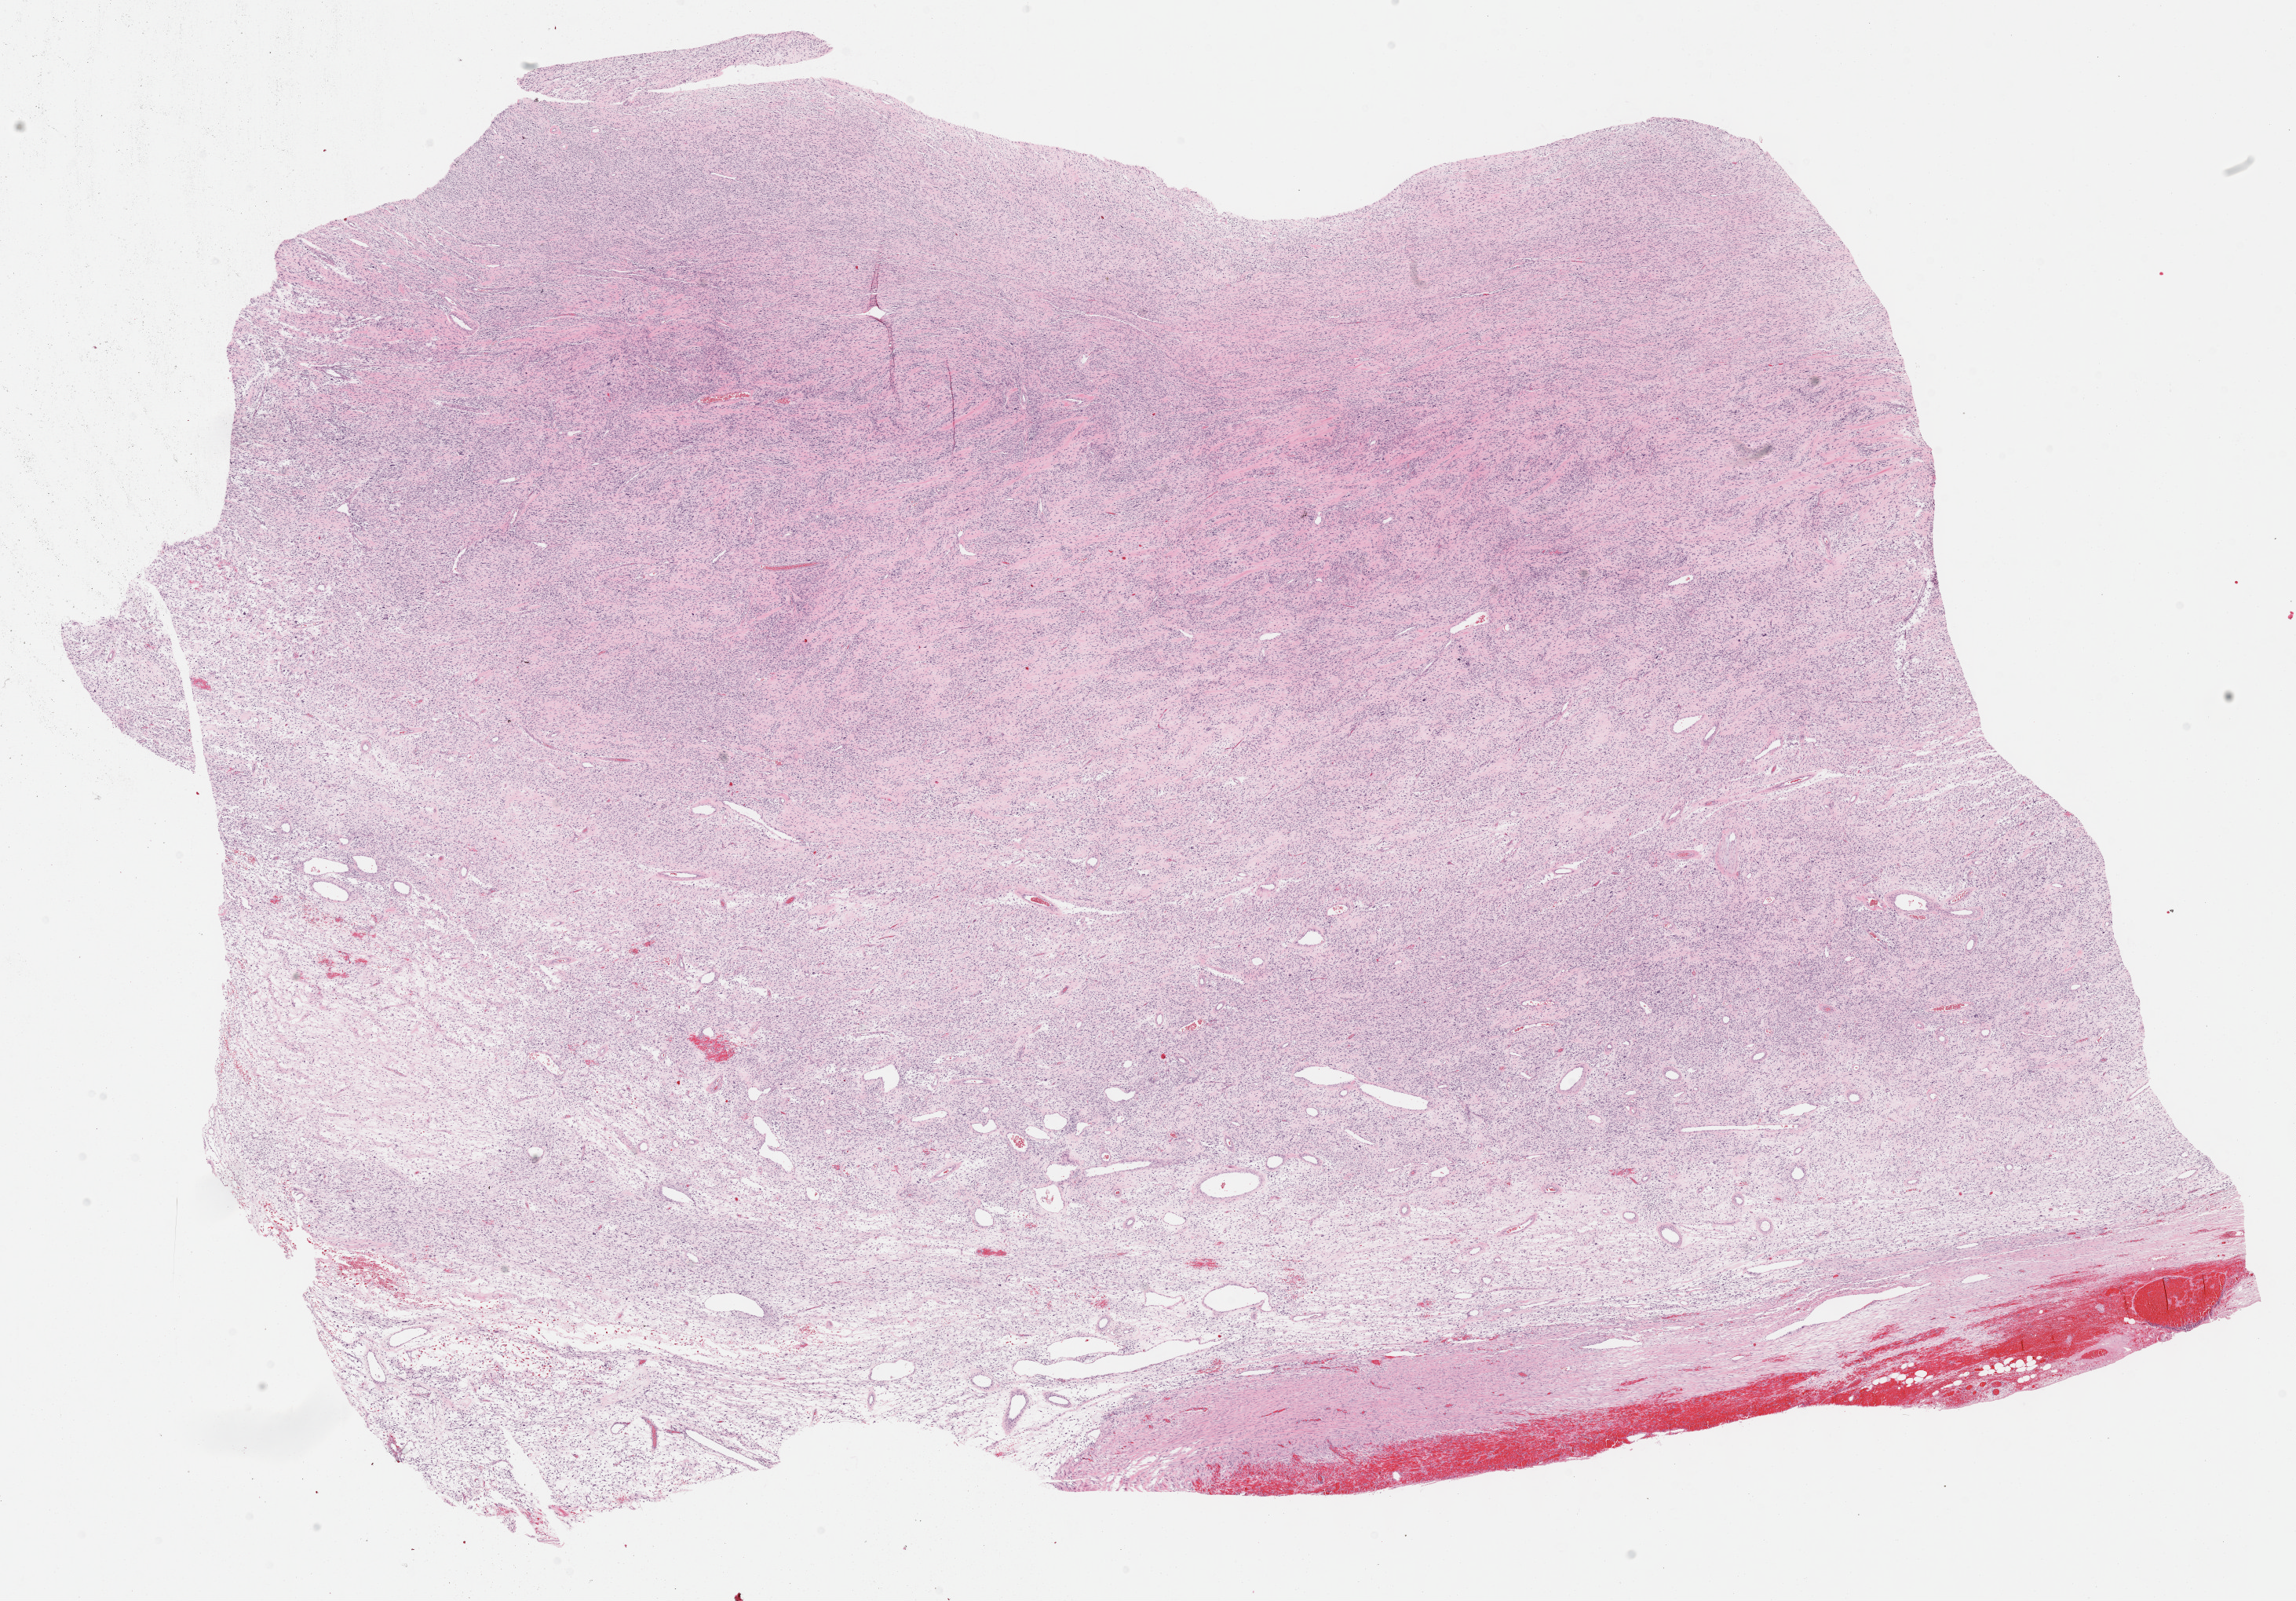
Whole-slide histology image, Hematoxylin and eosin (H&E) stained — shown as a low-resolution overview of the whole scanned area (about 23.7 x 16.5 mm). Formalin-fixed paraffin-embedded (FFPE) diagnostic section. Sample: primary tumour, retroperitoneum and peritoneum. Male patient; age at initial diagnosis 47 years.
• histologic diagnosis: Dedifferentiated liposarcoma